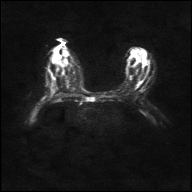
Breast MRI, one axial slice. Slice 16 of 36 in the series (ordered by position). Diffusion-weighted series; image 2 of 4 stored at this slice position (different b-values; order by instance number). 1.5 T. 192 × 192 image matrix. Female patient.
Structures marked on this image (expert manual segmentation):
- tumour on diffusion-weighted imaging: bounding box [x1, y1, x2, y2] px = [52, 87, 56, 91]